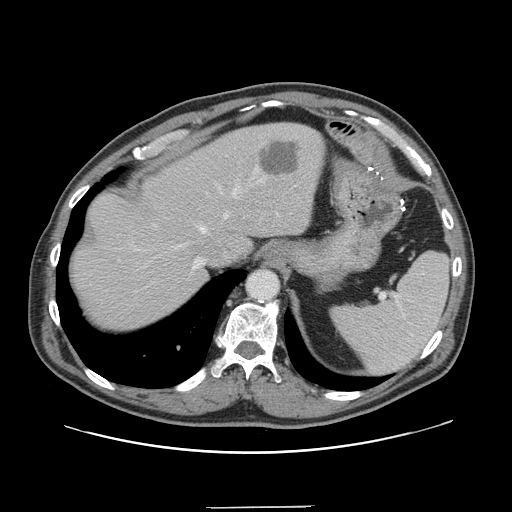
Contrast-enhanced abdominal CT, one axial slice; slice 117 of 139 in the series (ordered by position); 120 kVp; intravenous contrast given; soft-tissue window (W 400 / L 40 HU); 2.5 mm slice thickness; 512 × 512 image matrix. Male patient, age 64 years. From the clinical record (not read from this slice): diagnosis: colorectal cancer liver metastases, imaged before liver resection; multiple liver metastases: yes; largest metastasis: 3.5 cm; disease in both lobes: yes.
Outlined on this slice (manually delineated by an expert):
- hepatic veins: bounding box <180,180,263,269> (left, top, right, bottom; pixels)
- liver: <70,124,325,333>
- planned liver remnant (the part of the liver to remain after resection): <70,128,266,332>
- liver metastasis: <261,141,299,175>